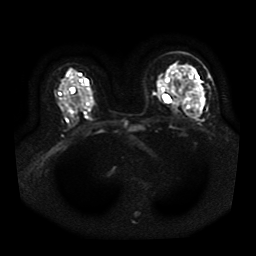
Breast MRI, one axial slice. Slice 24 of 41 in the series (ordered by position). Diffusion-weighted series; image 2 of 4 stored at this slice position (different b-values; order by instance number). 1.5 T. 5 mm slice thickness. 256 × 256 image matrix, field of view 330 × 330 mm. Female patient.
Structures marked on this image (expert manual segmentation):
- tumour on diffusion-weighted imaging: bounding box [x1, y1, x2, y2] px = [197, 90, 203, 104]